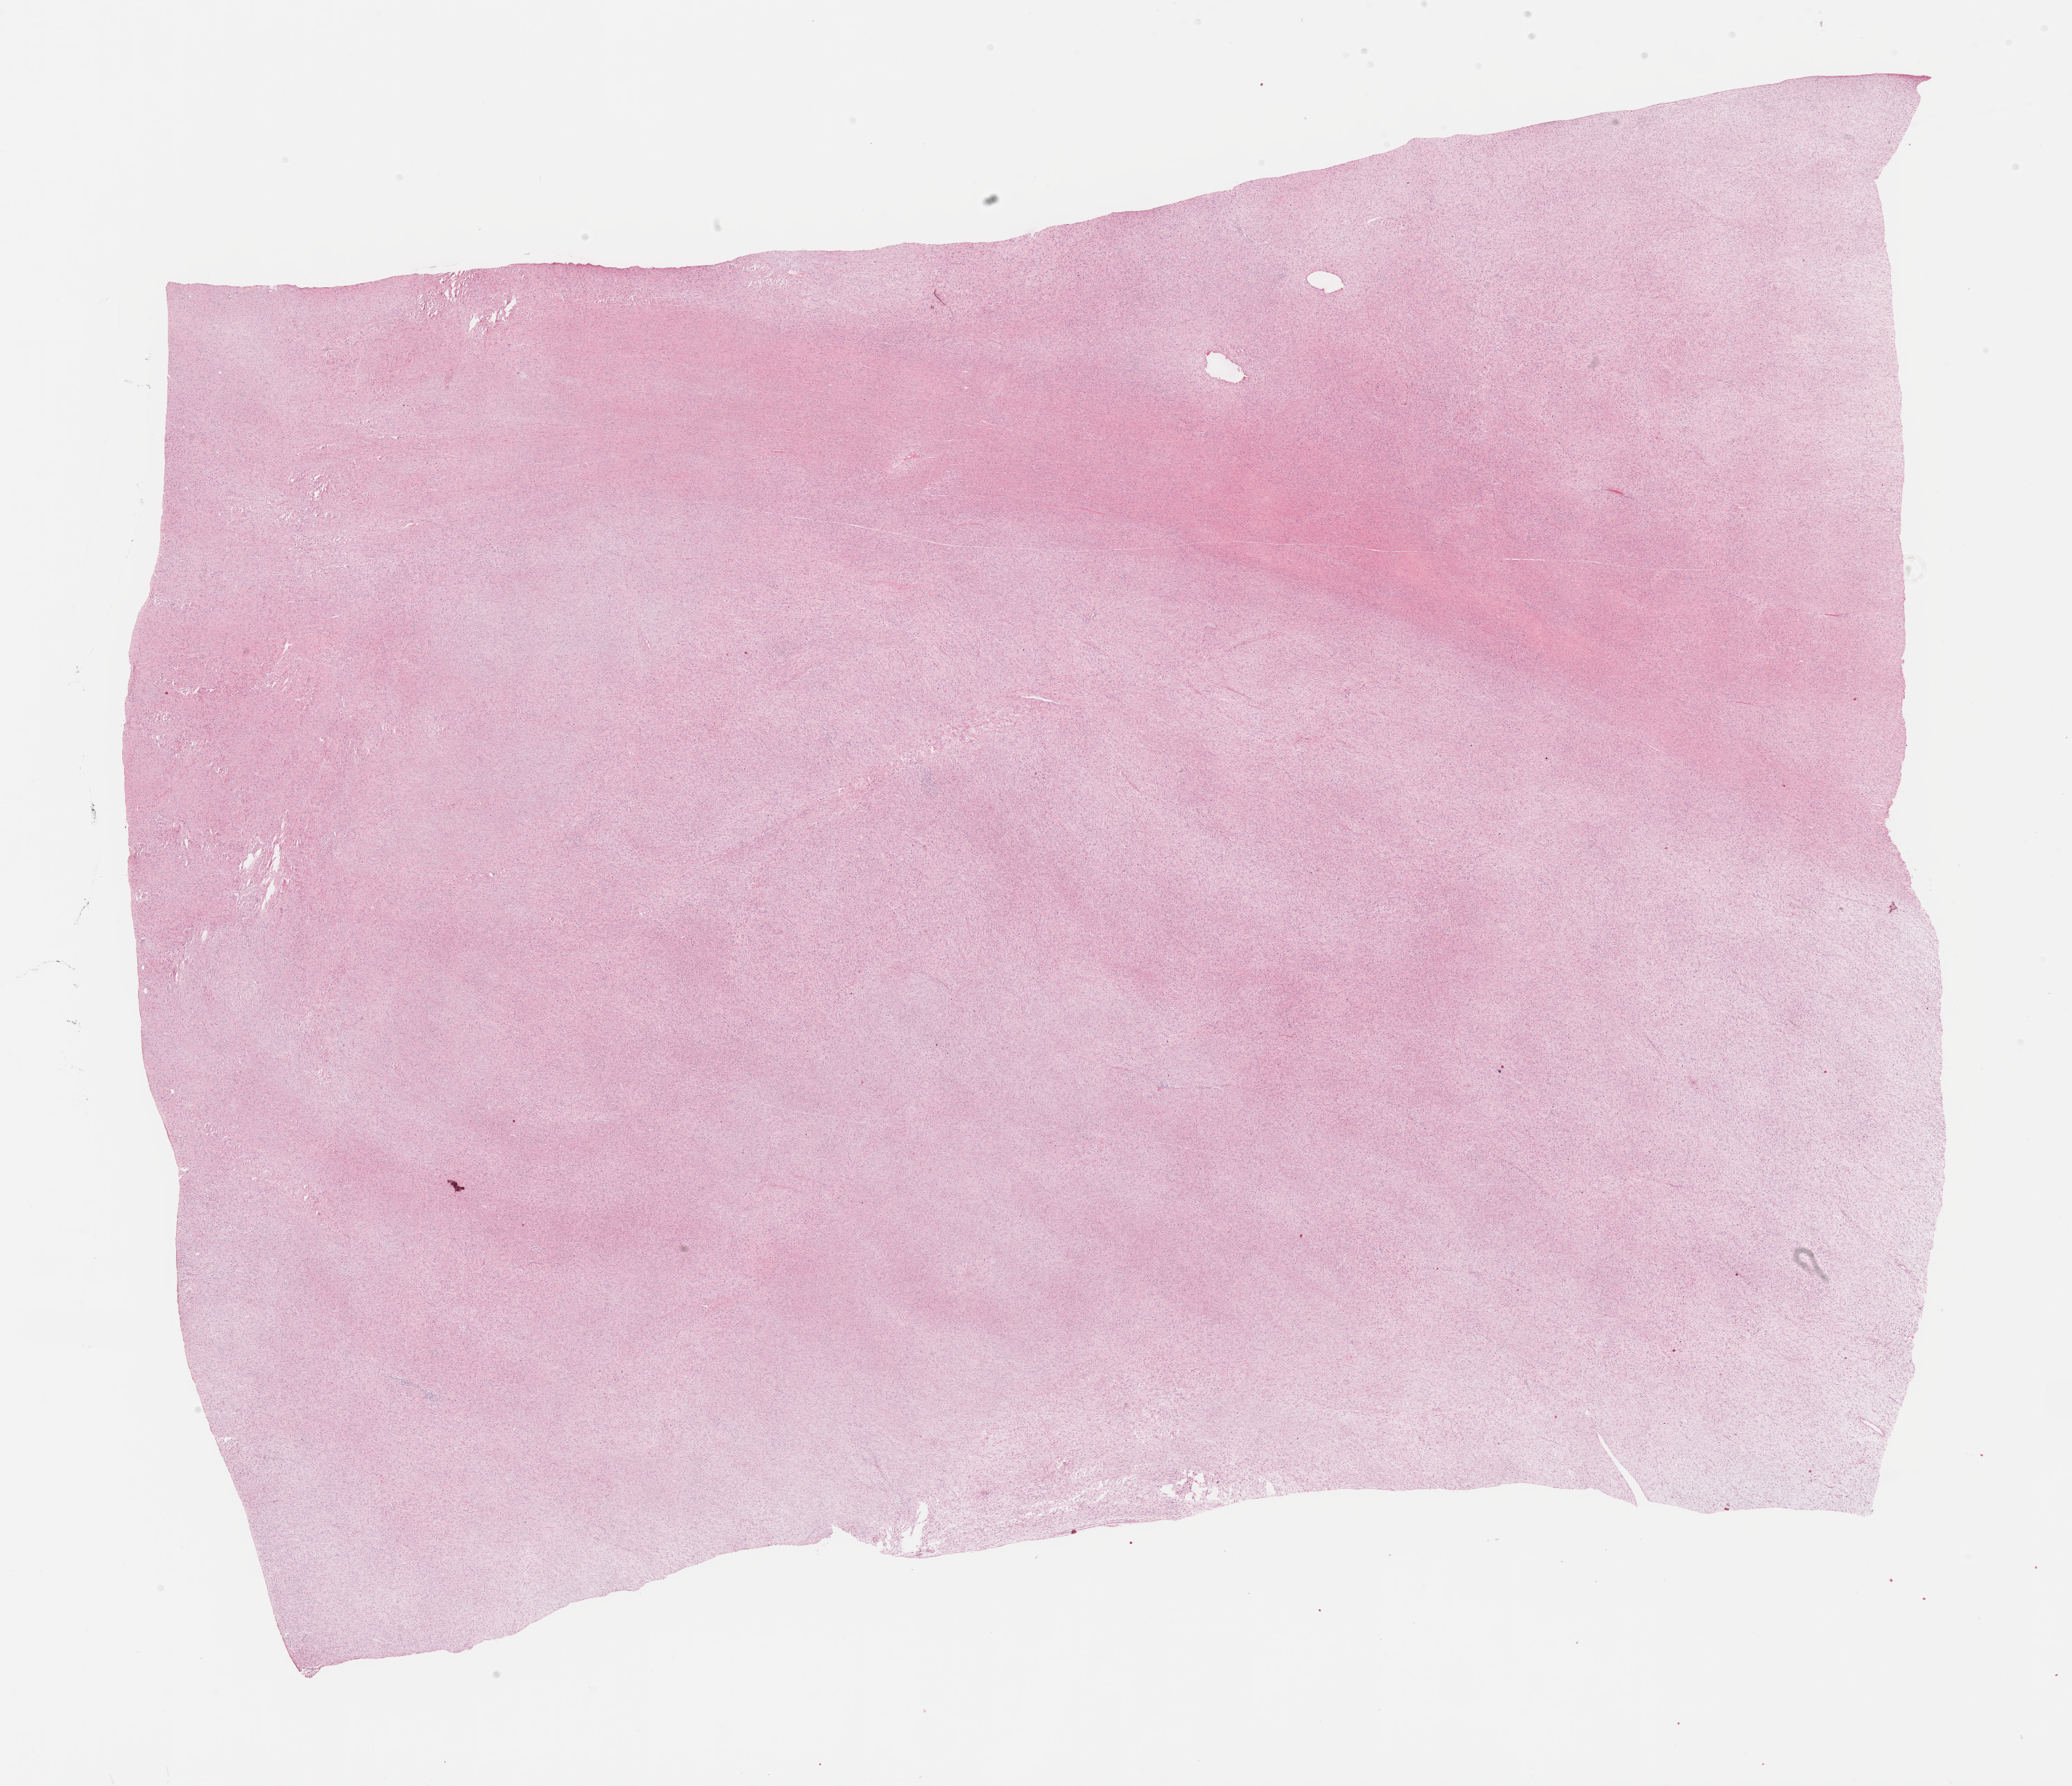
Digitized Hematoxylin and eosin (H&E) stained tissue section (whole slide) — a low-resolution overview of the entire scanned area, about 24.2 x 20.8 mm; formalin-fixed paraffin-embedded (FFPE) diagnostic section; sample: primary tumour, retroperitoneum and peritoneum. Female, age 60 years at initial diagnosis.
Histologic diagnosis: Dedifferentiated liposarcoma (retroperitoneum).